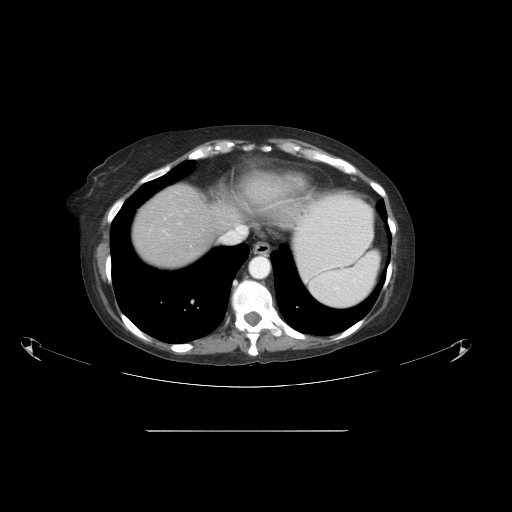
Contrast-enhanced abdominal CT, one axial slice. Slice 44 of 51 in the series (ordered by position). 120 kVp. Soft-tissue window (W 400 / L 40 HU). 512 × 512 image matrix, field of view 475 × 475 mm. Female patient, age 48 years. From the clinical record (not read from this slice): diagnosis: colorectal cancer liver metastases, imaged before liver resection; multiple liver metastases: yes; largest metastasis: 1 cm; disease in both lobes: no.
Outlined on this slice (expert manual segmentation):
- hepatic veins: bounding box <236,226,242,229> (left, top, right, bottom; pixels)
- liver: <132,172,292,270>
- planned liver remnant (the part of the liver to remain after resection): <133,184,223,270>